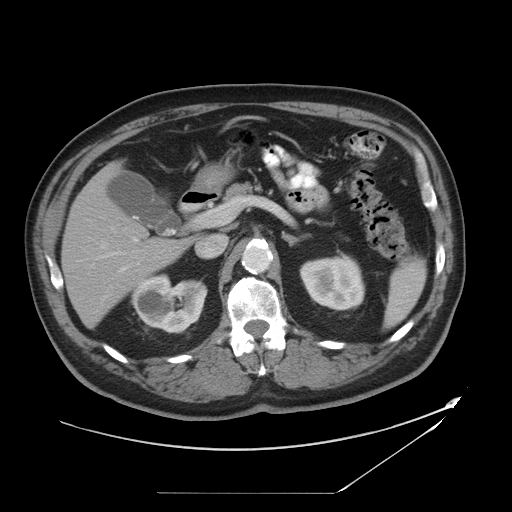
Contrast-enhanced abdominal CT, one axial slice; position 24 of 49 along the scan axis; intravenous contrast given; soft-tissue window (W 400 / L 40 HU); 5 mm slice thickness; 512 × 512 image matrix, field of view 461 × 461 mm. Male patient, age 72 years. From the clinical record (not read from this slice): diagnosis: colorectal cancer liver metastases, imaged before liver resection; multiple liver metastases: no.
Outlined on this slice (expert manual segmentation):
- hepatic veins: bounding box [x1, y1, x2, y2] px = [97, 227, 116, 249]
- liver: [63, 167, 186, 325]
- planned liver remnant (the part of the liver to remain after resection): [63, 168, 182, 325]
- portal vein (with intrahepatic branches): [97, 209, 216, 273]